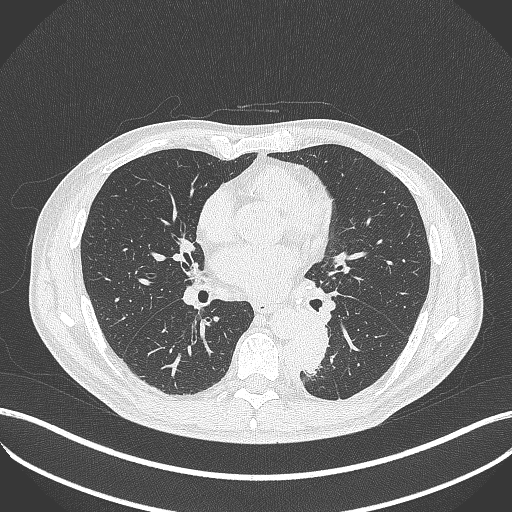
Chest CT, one axial slice; position 202 of 451 along the scan axis; reconstruction kernel B70f; 120 kVp; lung window (W 1500 / L -600 HU); 1 mm slice thickness; 512 × 512 image matrix. Male patient, age 72 years. Case-level facts recorded for this patient, not image findings: clinical TNM (as recorded): T2b N0 M1.
Outlined on this slice (rectangle marked by the reading radiologist):
- lung tumour (recorded histology: adenocarcinoma): bounding box (x1, y1, x2, y2) in pixels: (290, 319, 334, 378)